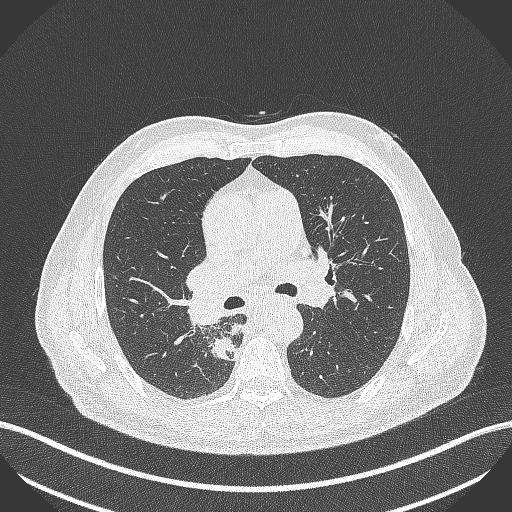
Chest CT, one axial slice; slice 278 of 451 in the series (ordered by position); reconstruction kernel B70f; 100 kVp; lung window (W 1500 / L -600 HU); 512 × 512 image matrix. Patient: male, 61 years. From the clinical record (not read from this slice): clinical TNM (as recorded): T1 N0 M0.
Outlined on this slice (rectangle marked by the reading radiologist):
- lung tumour (recorded histology: small cell carcinoma): box from (x=209, y=339) to (x=240, y=365) px